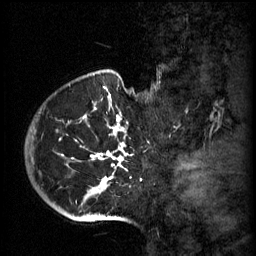
Breast MRI (dynamic contrast-enhanced), one sagittal slice. Slice 49 of 60 in the series (ordered by position). 3 images stored at this slice position (order not interpretable as contrast timing). 1.5 T. TE 4.2 ms, TR 11 ms. 2 mm slice thickness. 256 × 256 image matrix. Patient: female, 51 years.
Annotated regions visible in this slice (semi-automatically segmented with operator editing):
- analysis volume of interest (the breast-tissue region the enhancement analysis was run in; not a lesion): bounding box (x1, y1, x2, y2) in pixels: (48, 82, 153, 197)
- tumour enhancement mask (voxels above the 70 % enhancement threshold inside the analysis volume of interest): (62, 96, 133, 189)